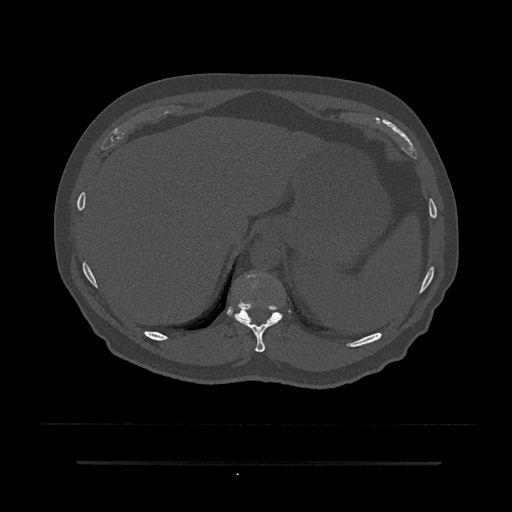
CT including the spine, one axial slice; position 300 of 797 along the scan axis; 120 kVp; bone window (W 1800 / L 400 HU); 0.5 mm slice thickness; 512 × 512 image matrix, field of view 464 × 464 mm. Male patient, age 59 years. Case-level facts recorded for this patient, not image findings: primary cancer: bile ducts.
Outlined on this slice (semi-automatically segmented with operator editing):
- T10 vertebra: bounding box (x1, y1, x2, y2) in pixels: (235, 316, 283, 353)
- T11 vertebra: (228, 302, 283, 321)